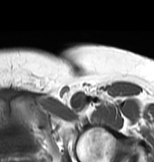
MRI of an extremity soft-tissue mass, one axial slice; position 61 of 83 along the scan axis; MR volume resampled by the dataset authors to the PET/CT grid (not the native acquisition matrix); 3.27 mm slice thickness; 154 × 162 image matrix, field of view 150 × 158 mm. Female patient. From the clinical record (not read from this slice): histological type: myxofibrosarcoma; grade: intermediate; site of the primary tumour: left thigh.
Outlined on this slice (expert contour drawn on MRI and transferred to this co-registered scan by the dataset authors):
- gross tumour volume including surrounding oedema: bounding box (x1, y1, x2, y2) in pixels: (67, 93, 91, 115)